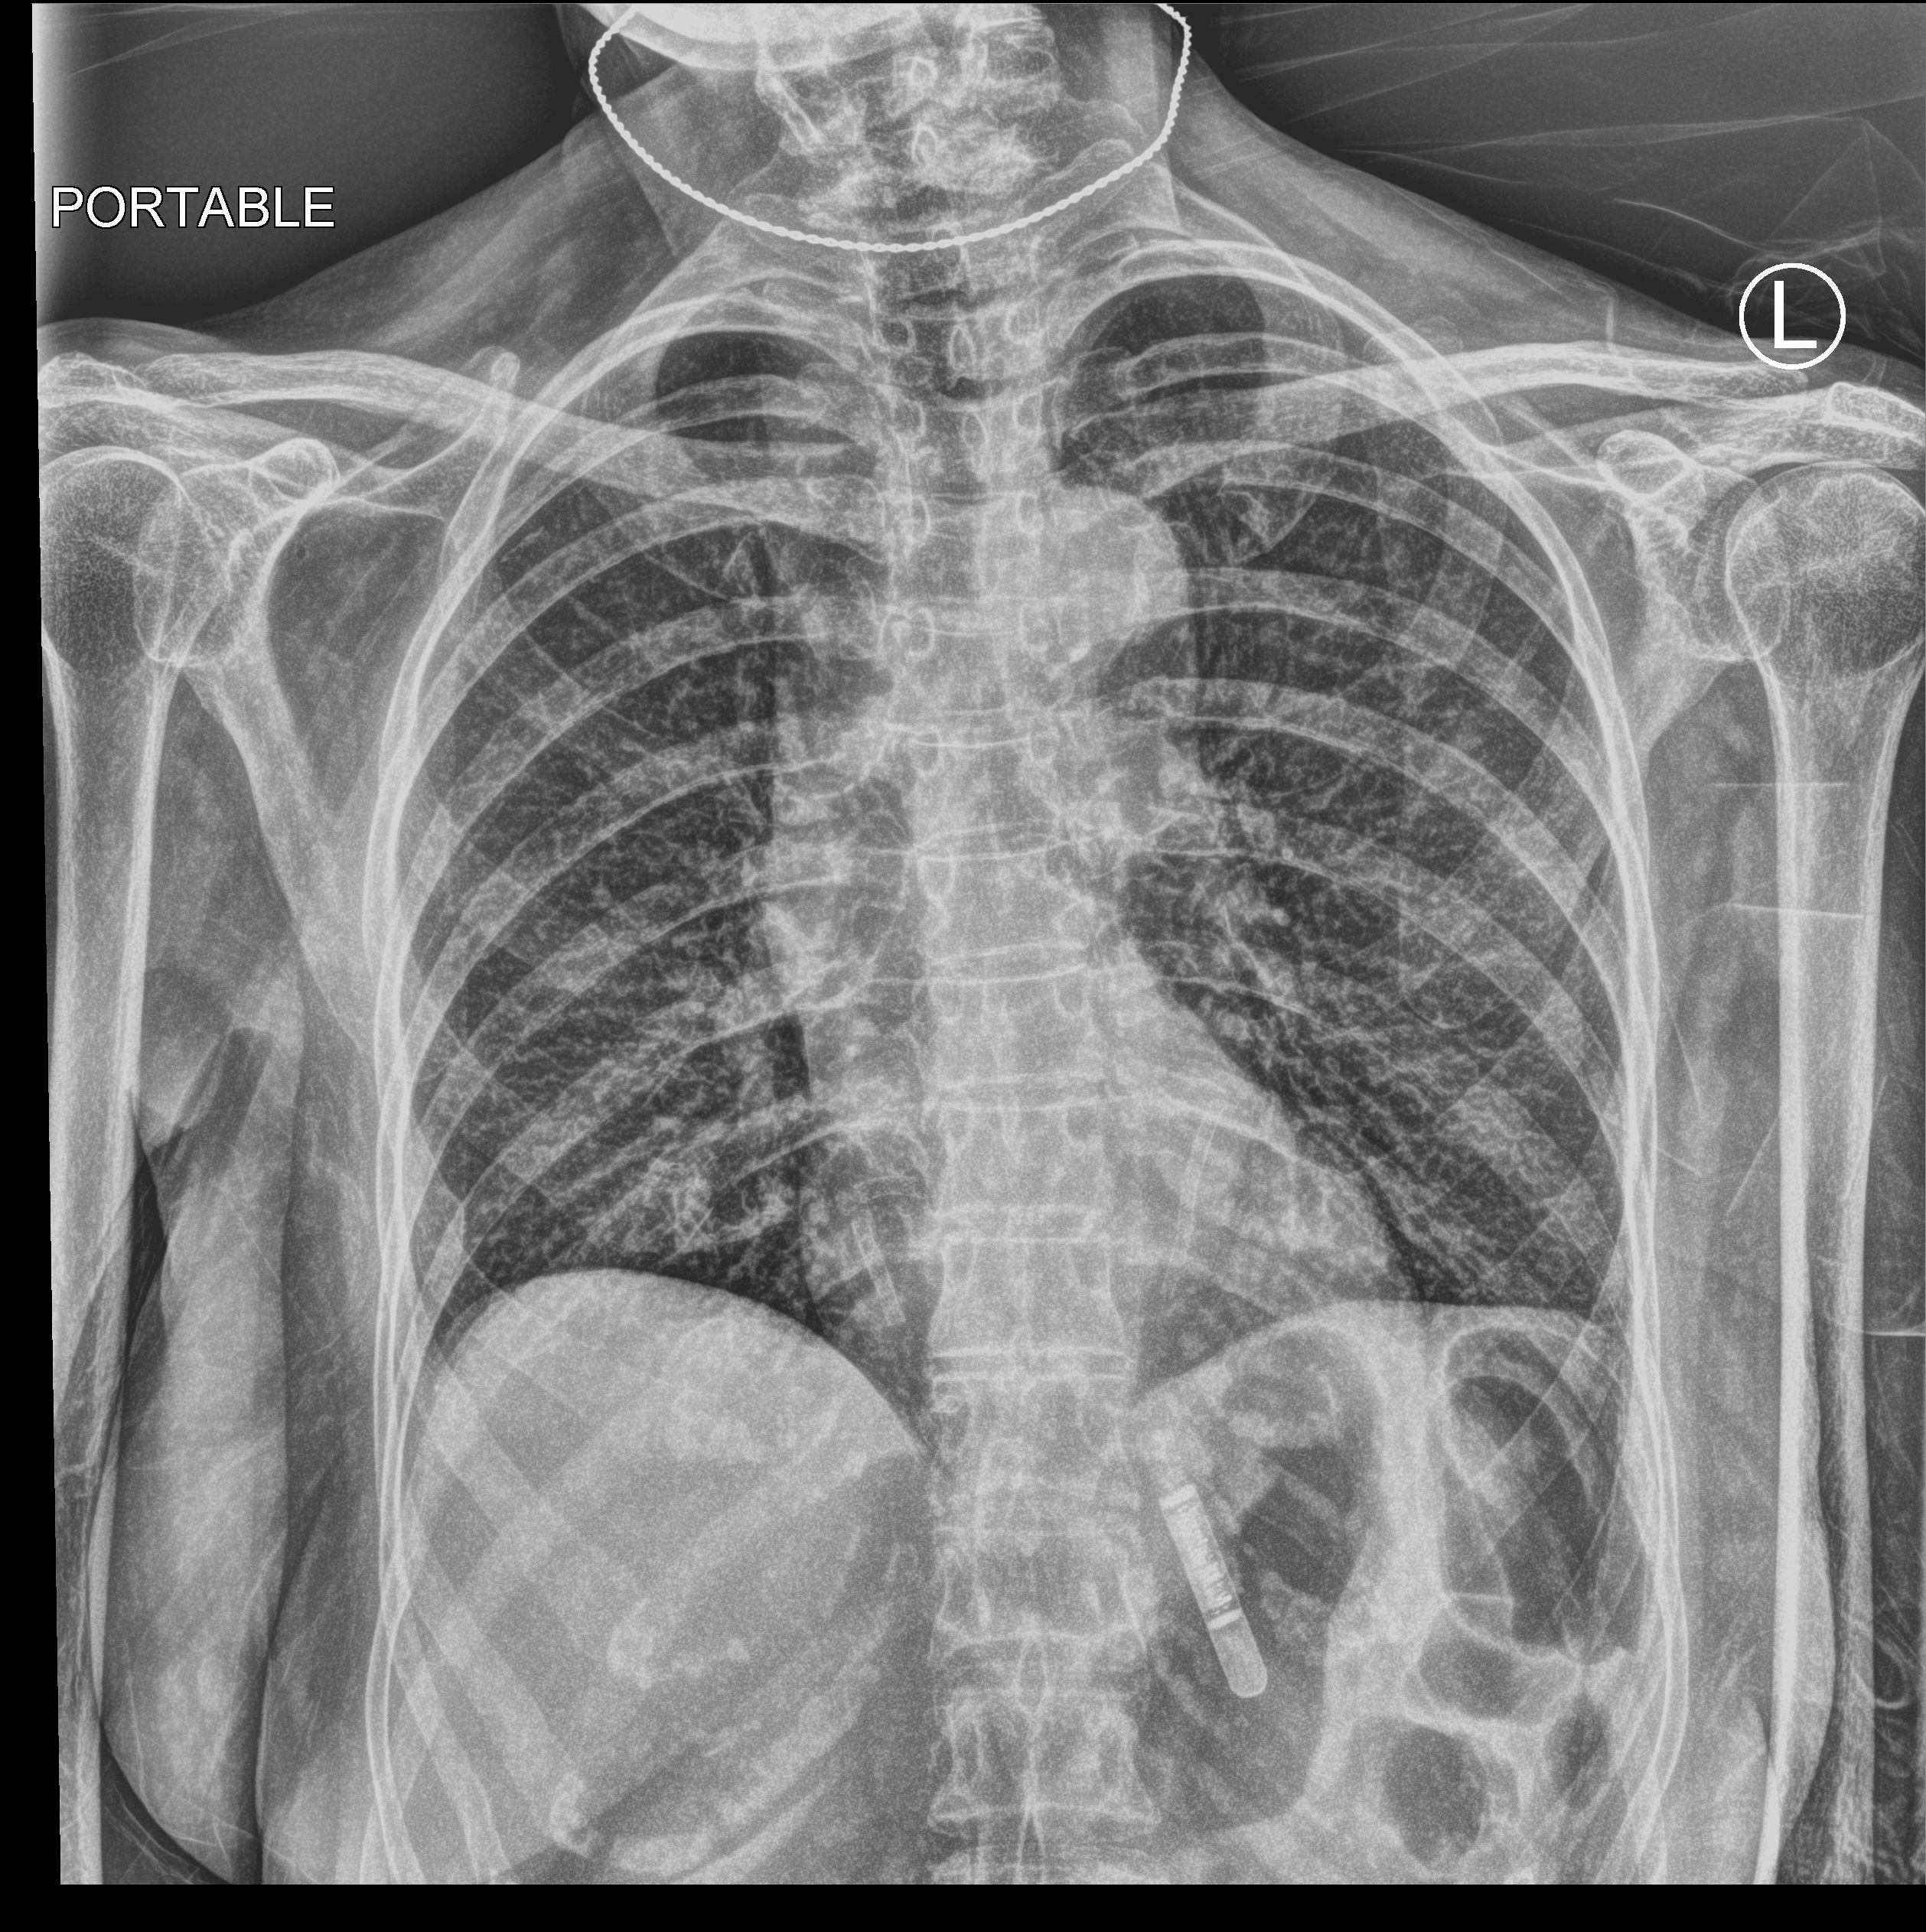
Chest X-ray (portable), anteroposterior (AP) projection. Patient hospitalised with COVID-19; female, aged 60–74 years.
Admission-level facts for this patient (not findings on this image; timing relative to this image not recorded): hypertension (admission record): yes; mechanically ventilated during this hospital stay: no.